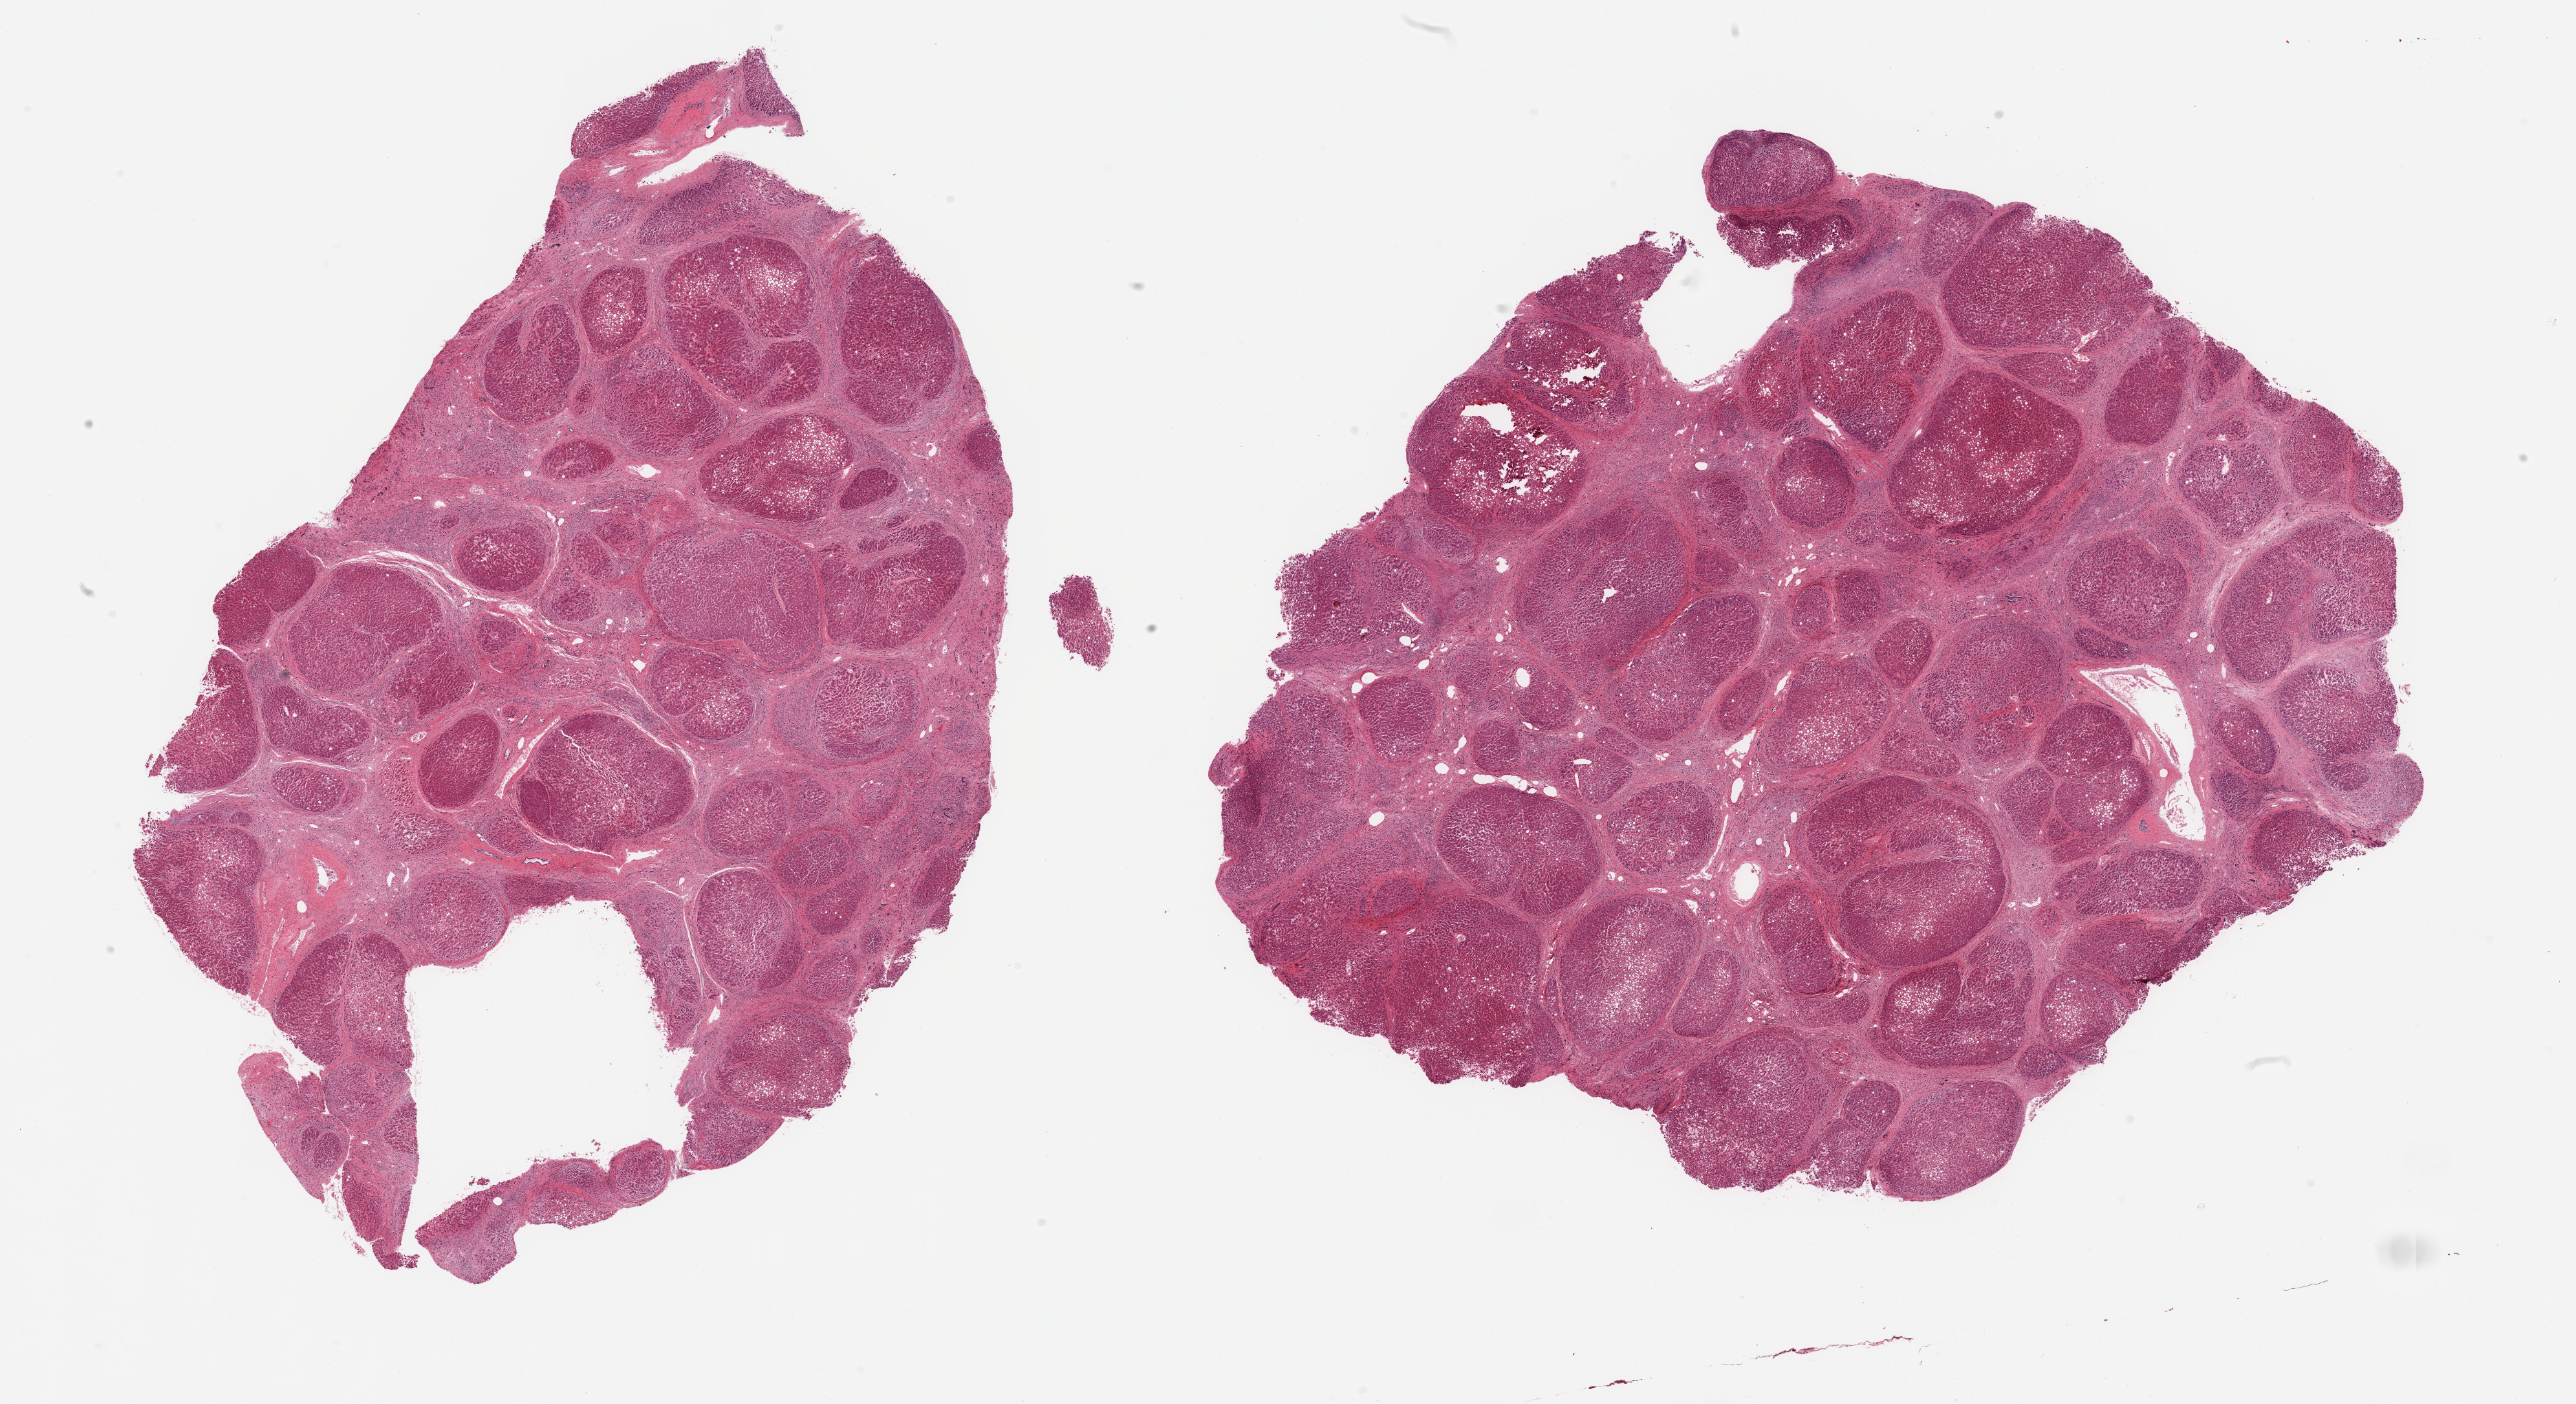
Haematoxylin and eosin whole-slide image, shown as a low-resolution overview of the whole scanned area (about 31.5 x 17.2 mm, acquisition: 20x scan); PAXgene-fixed, paraffin-embedded tissue; sampled site (target tissue): liver; donor tissue sample. Donor: male.
Reviewer comment on this tissue sample: 2 pieces; advanced portal cirrhosis and steatosis.